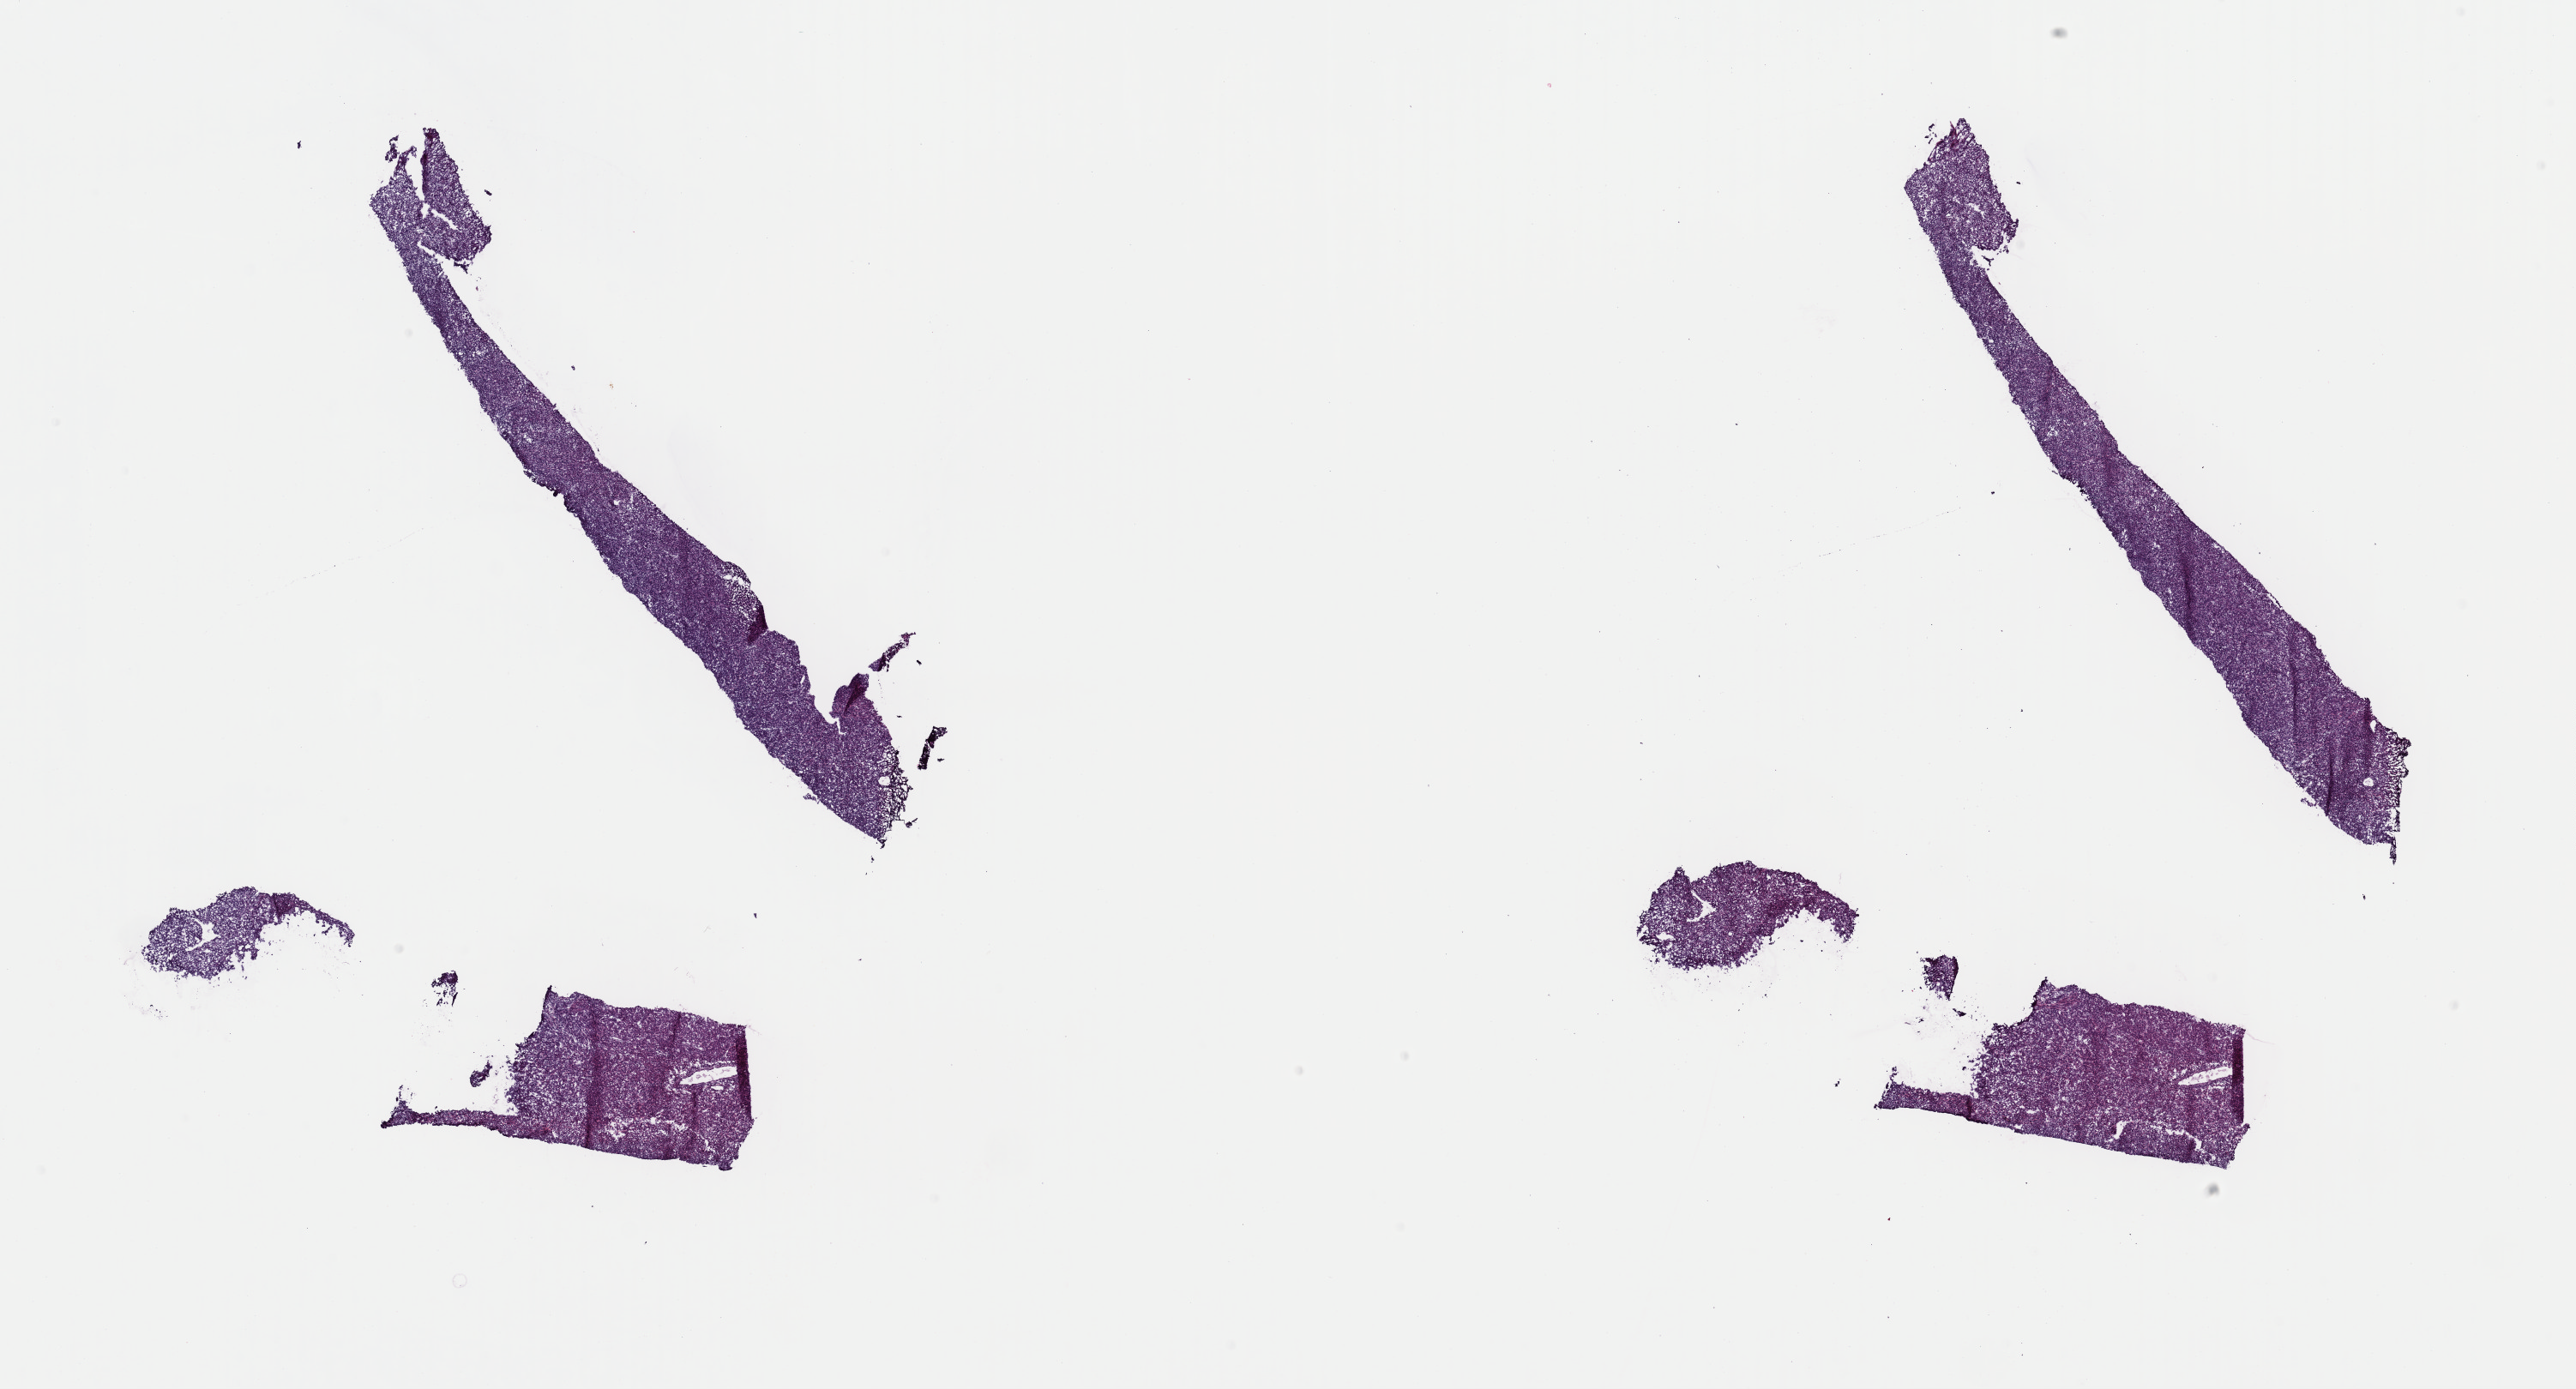
H&E-stained whole-slide image — whole scanned area (about 23.7 x 12.8 mm) shown as a low-resolution overview; frozen section; uterus, primary tumour sample. Female patient; age at initial diagnosis 56 years. Pathologist review of this section (percent, as recorded): tumour cells 95%, tumour nuclei 100%, normal cells 0%, stromal cells 5%, necrosis 0%. Infiltration values recorded for this section: lymphocyte infiltration 0%, monocyte infiltration 0%, neutrophil infiltration 0%.
Pathologic diagnosis: Leiomyosarcoma, NOS.